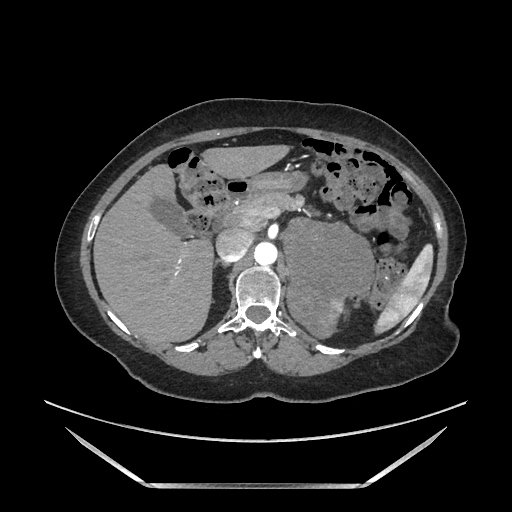
Contrast-enhanced abdominal CT, one axial slice. Soft-tissue window (W 400 / L 40 HU). 512 × 512 image matrix, field of view 440 × 440 mm. Female patient. Case-level facts recorded for this patient, not image findings: diagnosis: adrenocortical carcinoma; tumour side: left adrenal; tumour size at pathology: 12.5 cm; Ki-67 index: 39 %; stage (as recorded): 3.
Annotated regions visible in this slice (semi-automatic segmentation, software-assisted and operator-edited):
- mass: box from (x=286, y=221) to (x=373, y=335) px